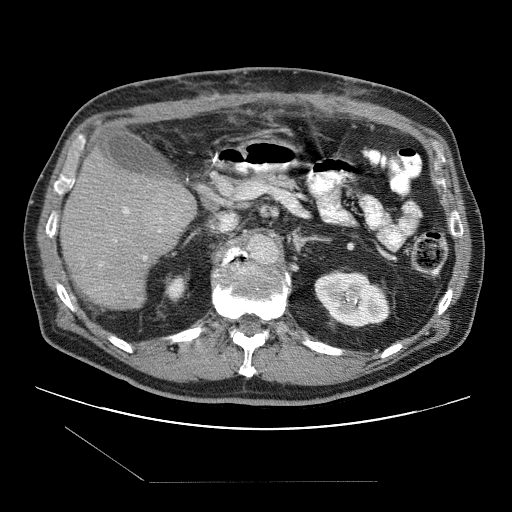
Contrast-enhanced abdominal CT (liver protocol), one axial slice; position 48 of 109 along the scan axis; reconstruction kernel STANDARD; one of 2 acquisitions stored at this slice position; soft-tissue window (W 400 / L 40 HU); 2.5 mm slice thickness; 512 × 512 image matrix, field of view 400 × 400 mm. Case-level facts recorded for this patient, not image findings: diagnosis: hepatocellular carcinoma (patient treated with transarterial chemoembolisation; whether this scan precedes or follows treatment is not stated here); TNM stage (as recorded): Stage-IIIB; Child-Pugh class: A.
Annotated regions visible in this slice (semi-automatically segmented with operator editing):
- liver parenchyma outside the tumour (the mass and vessels are separate outlines, so this box may not span the whole liver): box from (x=60, y=148) to (x=196, y=308) px
- liver vessels: (x=114, y=207)–(x=162, y=259)